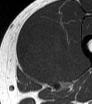
MRI of an extremity soft-tissue mass, one axial slice. Position 27 of 62 along the scan axis. MR volume resampled by the dataset authors to the PET/CT grid (not the native acquisition matrix). 3.27 mm slice thickness. 92 × 104 image matrix, field of view 90 × 102 mm. Male patient. Case-level facts recorded for this patient, not image findings: histological type: mixoid liposarcoma; grade: low; site of the primary tumour: left thigh.
Structures marked on this image (expert contour drawn on MRI and transferred to this co-registered scan by the dataset authors):
- gross tumour volume (mass): bounding box <19,22,68,82> (left, top, right, bottom; pixels)